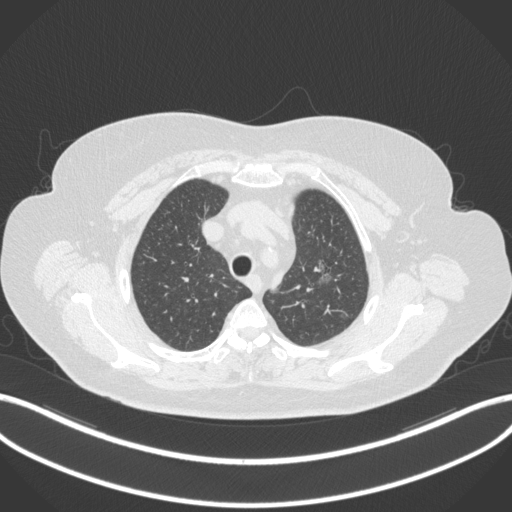
Chest CT, one axial slice. Reconstruction kernel B31f. Lung window (W 1500 / L -600 HU). 1 mm slice thickness. 512 × 512 image matrix. Patient: female, 70 years. From the clinical record (not read from this slice): clinical TNM (as recorded): T1c N0 M0.
Outlined on this slice (rectangle marked by the reading radiologist):
- lung tumour (recorded histology: adenocarcinoma): bounding box [x1, y1, x2, y2] px = [309, 256, 337, 293]